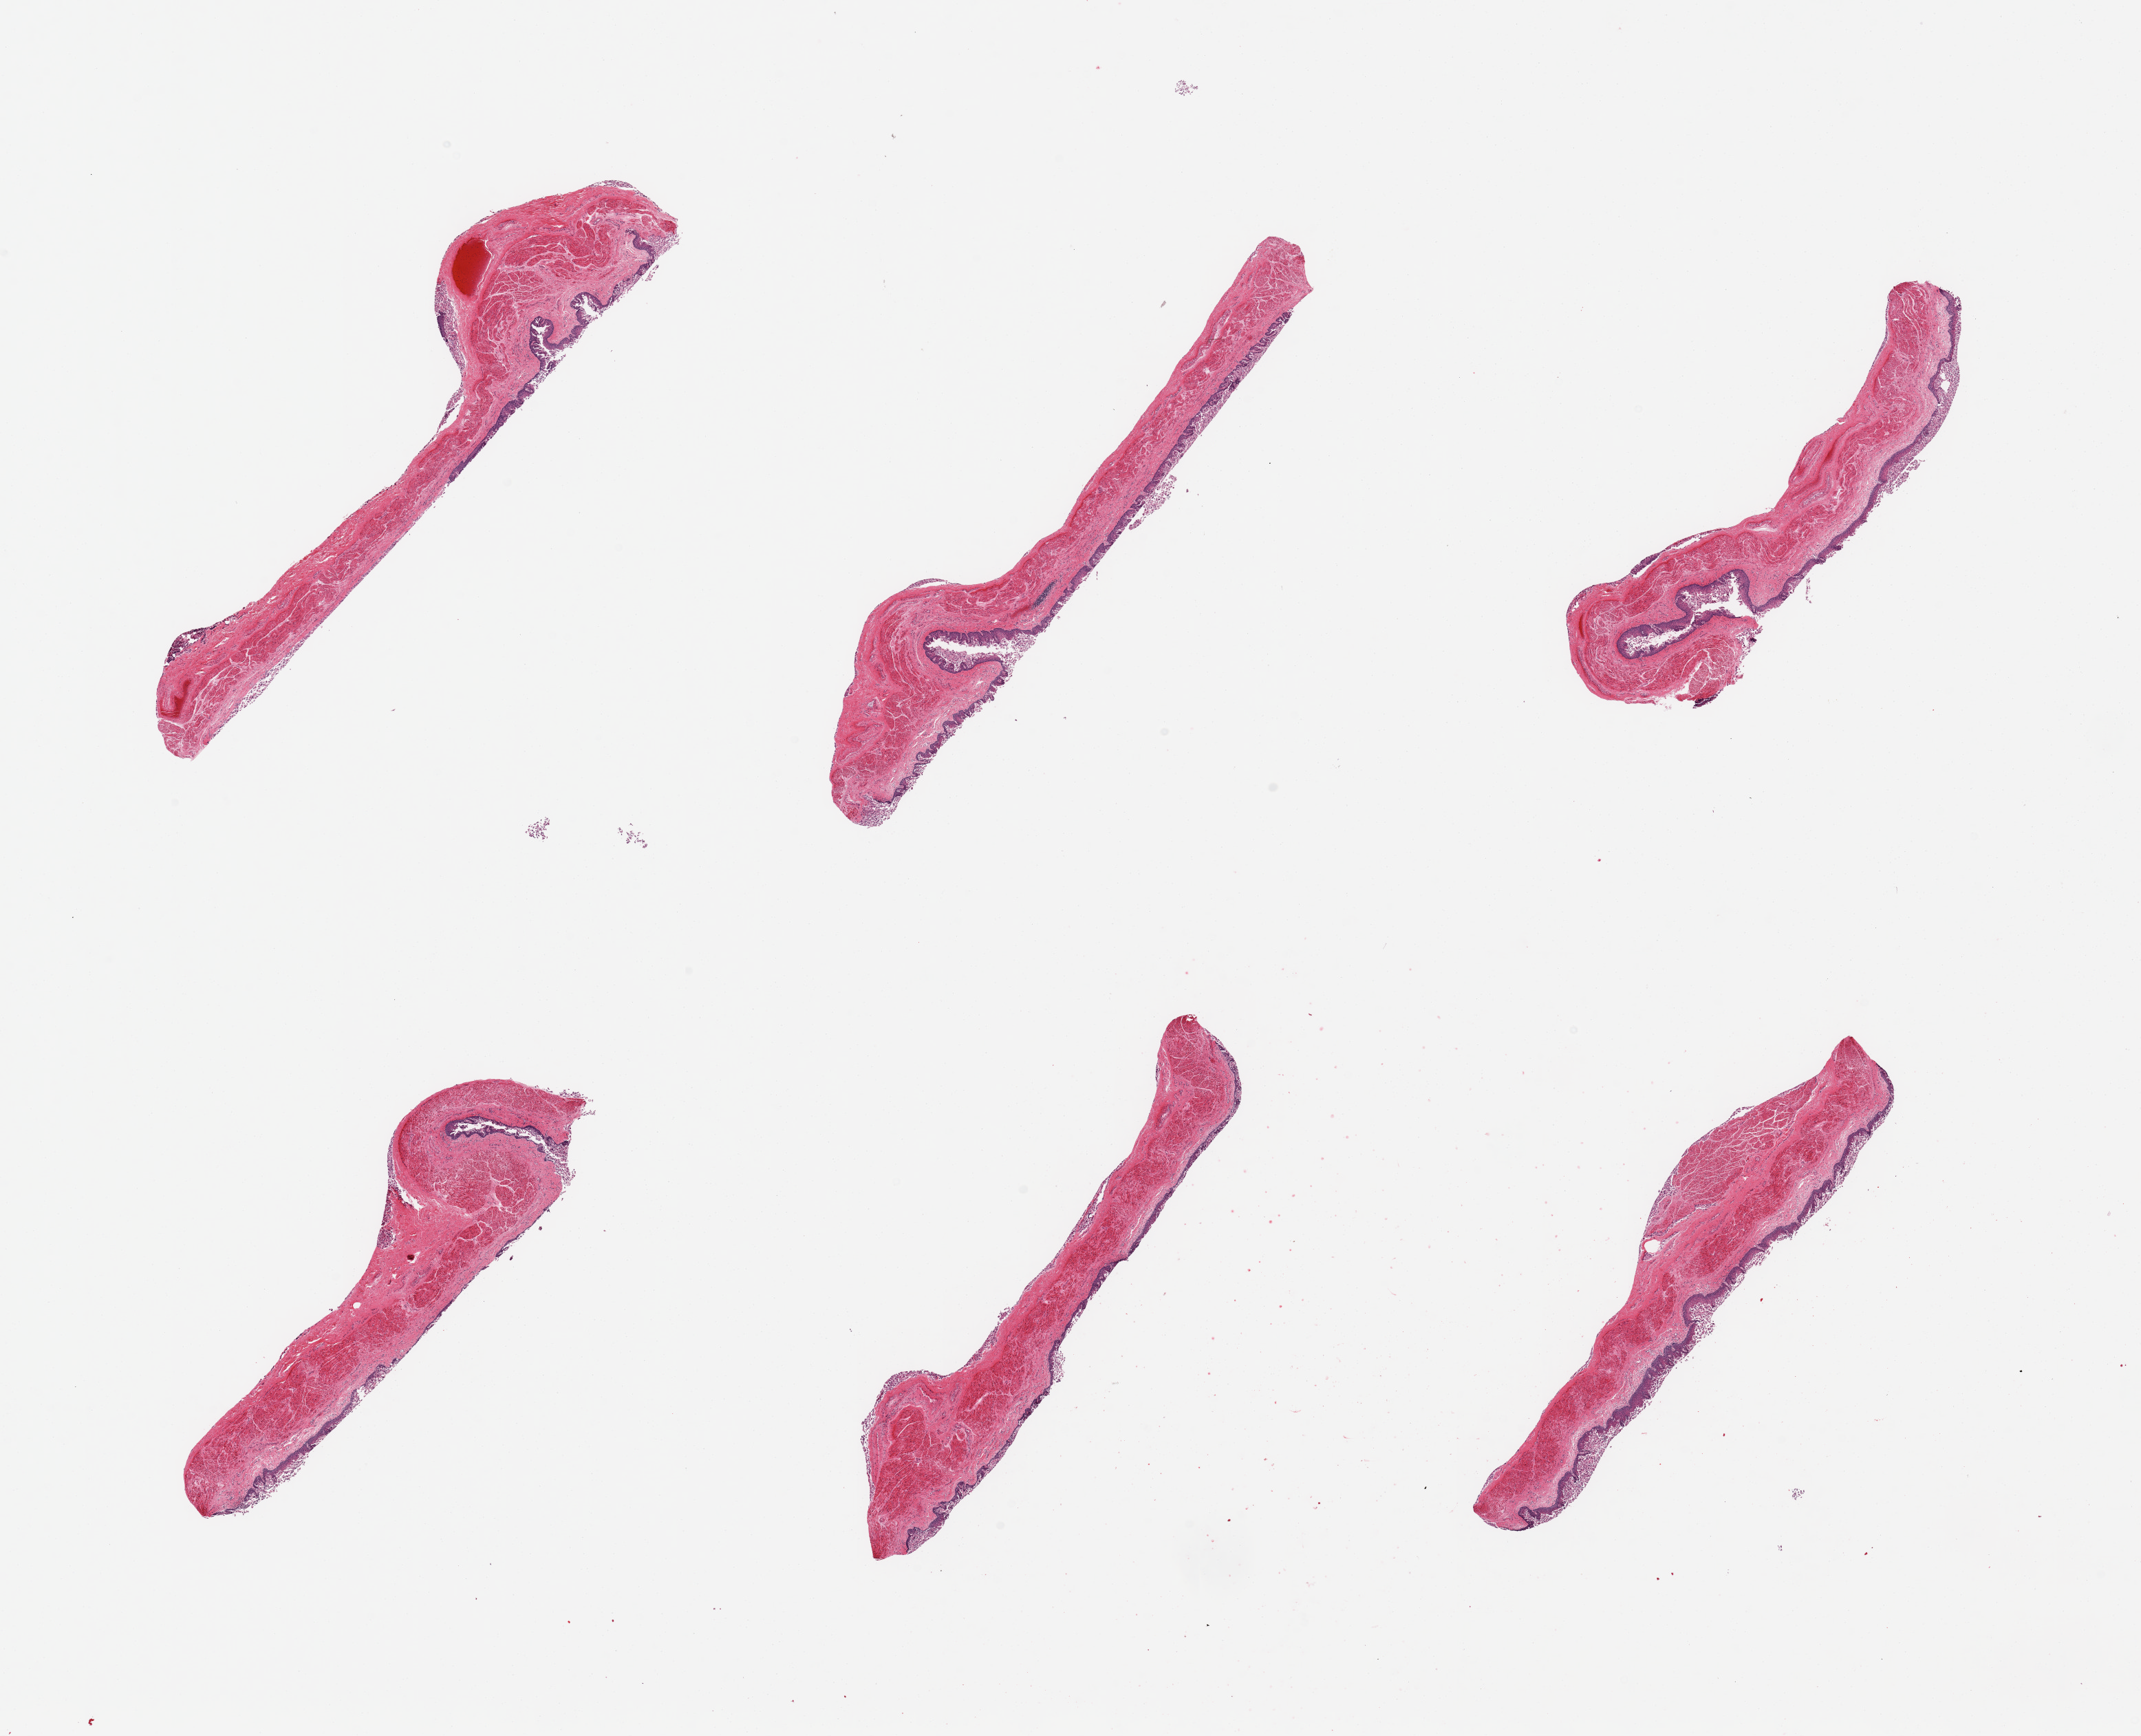
Haematoxylin and eosin whole-slide image — shown as a low-resolution overview of the whole scanned area (about 24.6 x 20.0 mm); PAXgene-fixed, paraffin-embedded tissue; sampled site (target tissue): esophageal mucous membrane; donor tissue sample.
Reviewer comment on this tissue sample: 6 pieces; epithelium is sloughing, one piece includes small portion of muscularis (not target).